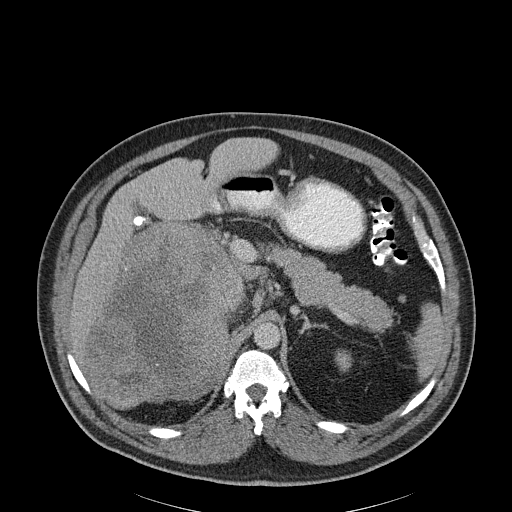
Contrast-enhanced abdominal CT, one axial slice; position 136 of 186 along the scan axis; 120 kVp; soft-tissue window (W 400 / L 40 HU); 512 × 512 image matrix, field of view 464 × 464 mm. Patient: male, 56 years. Case-level facts recorded for this patient, not image findings: diagnosis: adrenocortical carcinoma; tumour side: right adrenal; tumour size at pathology: 18 cm; Ki-67 index: 2 %; stage (as recorded): 3.
Outlined on this slice (semi-automatically segmented with operator editing):
- mass: box from (x=88, y=223) to (x=241, y=406) px